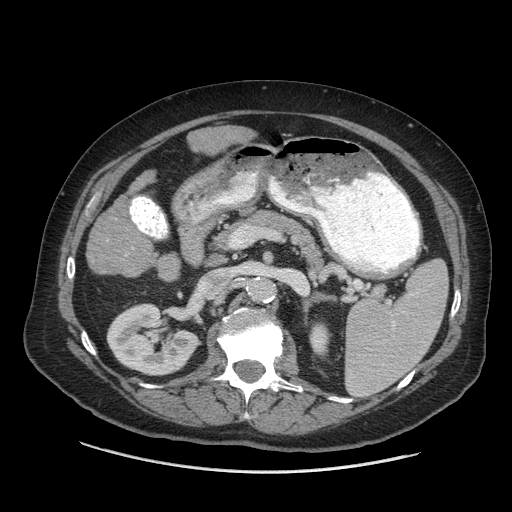
Contrast-enhanced abdominal CT (liver protocol), one axial slice. Soft-tissue window (W 400 / L 40 HU). 2.5 mm slice thickness. 512 × 512 image matrix, field of view 420 × 420 mm. From the clinical record (not read from this slice): diagnosis: hepatocellular carcinoma (patient treated with transarterial chemoembolisation; whether this scan precedes or follows treatment is not stated here); TNM stage (as recorded): Stage-I; Child-Pugh class: A.
Structures marked on this image (semi-automatically segmented with operator editing):
- liver parenchyma outside the tumour (the mass and vessels are separate outlines, so this box may not span the whole liver): bounding box (x1, y1, x2, y2) in pixels: (86, 126, 252, 280)